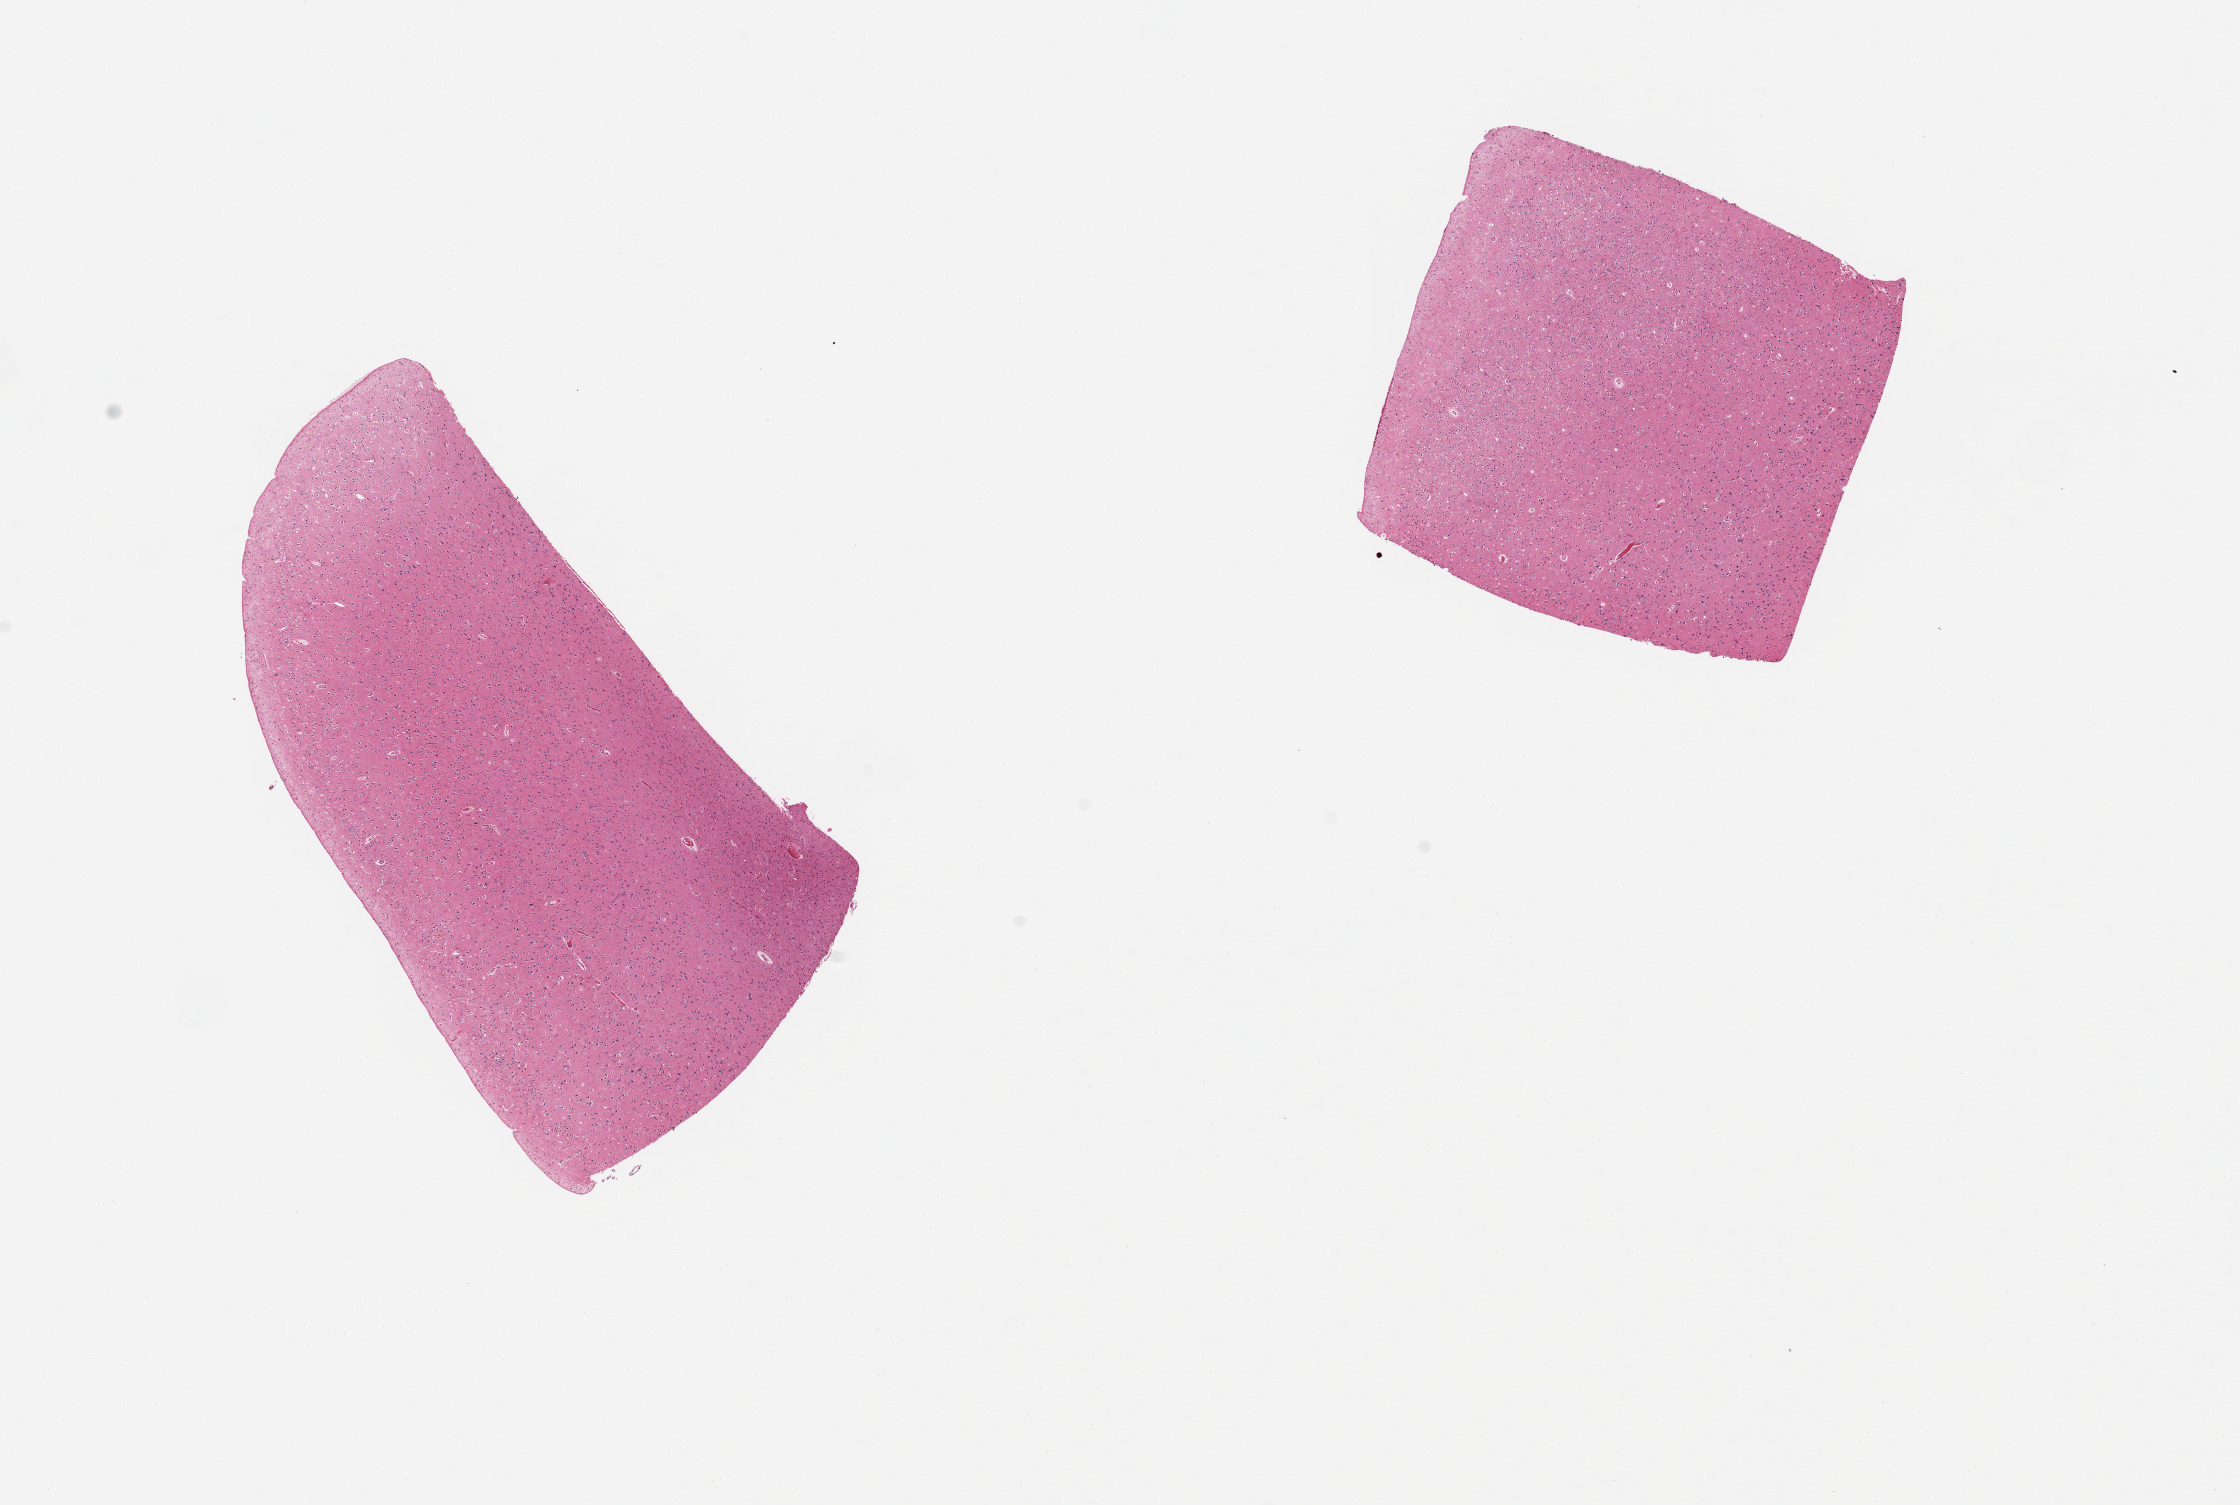
Whole-slide image, hematoxylin and eosin (H&E) stain — low-resolution overview of the scanned area, about 17.7 x 11.9 mm. PAXgene-fixed, paraffin-embedded tissue. Target tissue: cerebral cortex. Tissue donor sample. Male donor.
• reviewer comment on this tissue sample: 2 pieces, no abnormalities